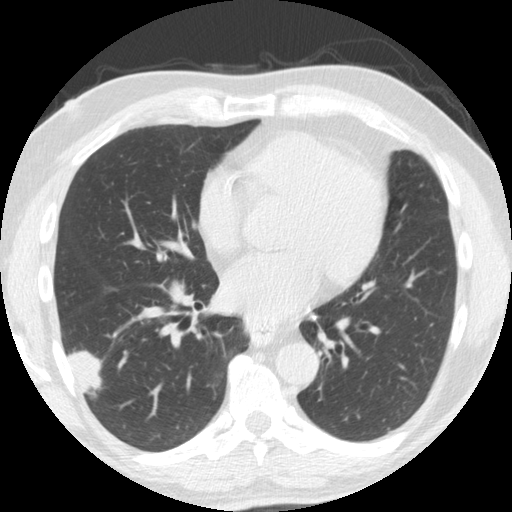
Low-dose screening chest CT, one axial slice. Slice 77 of 174 in the series (ordered by position). 120 kVp. Lung window (W 1500 / L -600 HU). 512 × 512 image matrix, field of view 341 × 341 mm.
Structures marked on this image (outlined manually by an expert reader):
- lesion 1 (tumor, lower lobe of right lung): bounding box (x1, y1, x2, y2) in pixels: (68, 351, 102, 392)